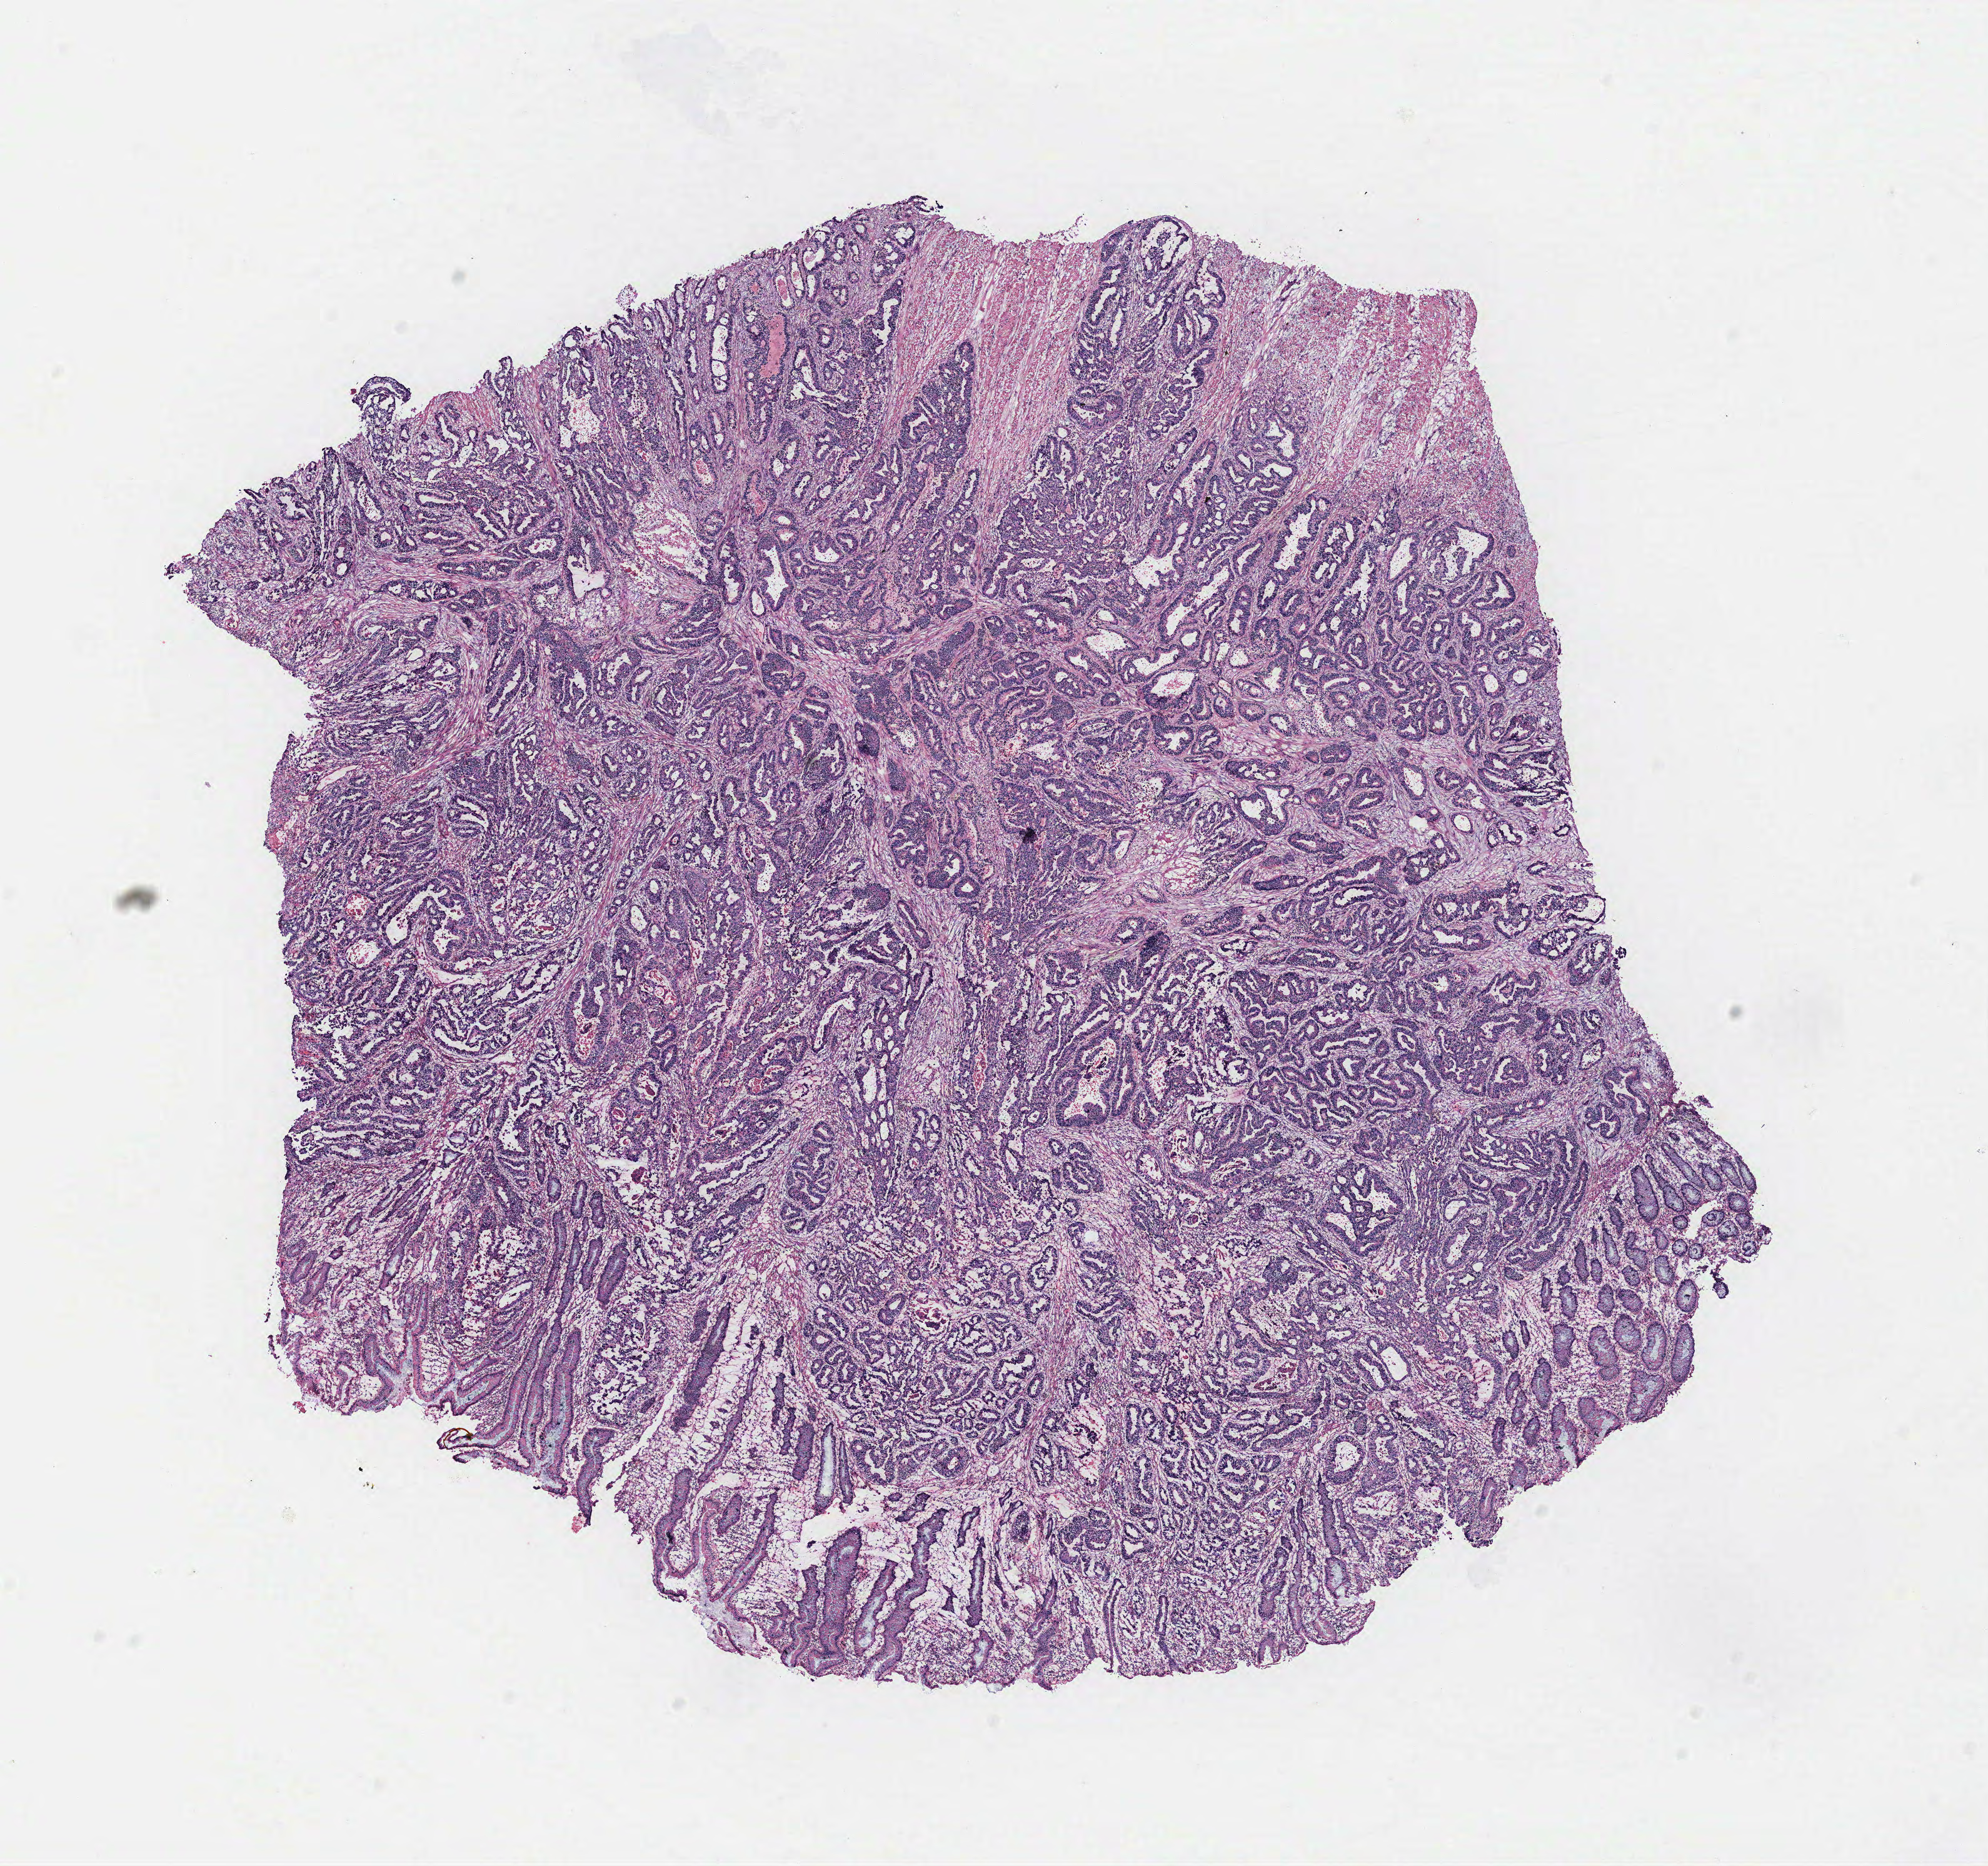
H&E whole-slide image, low-resolution overview of the scanned area, about 12.7 x 11.9 mm. Normal (non-tumour) tissue sample, colon. 64-year-old female patient.
- this section: normal (non-tumour) tissue from the same patient
- patient diagnosis: Adenocarcinoma, NOS